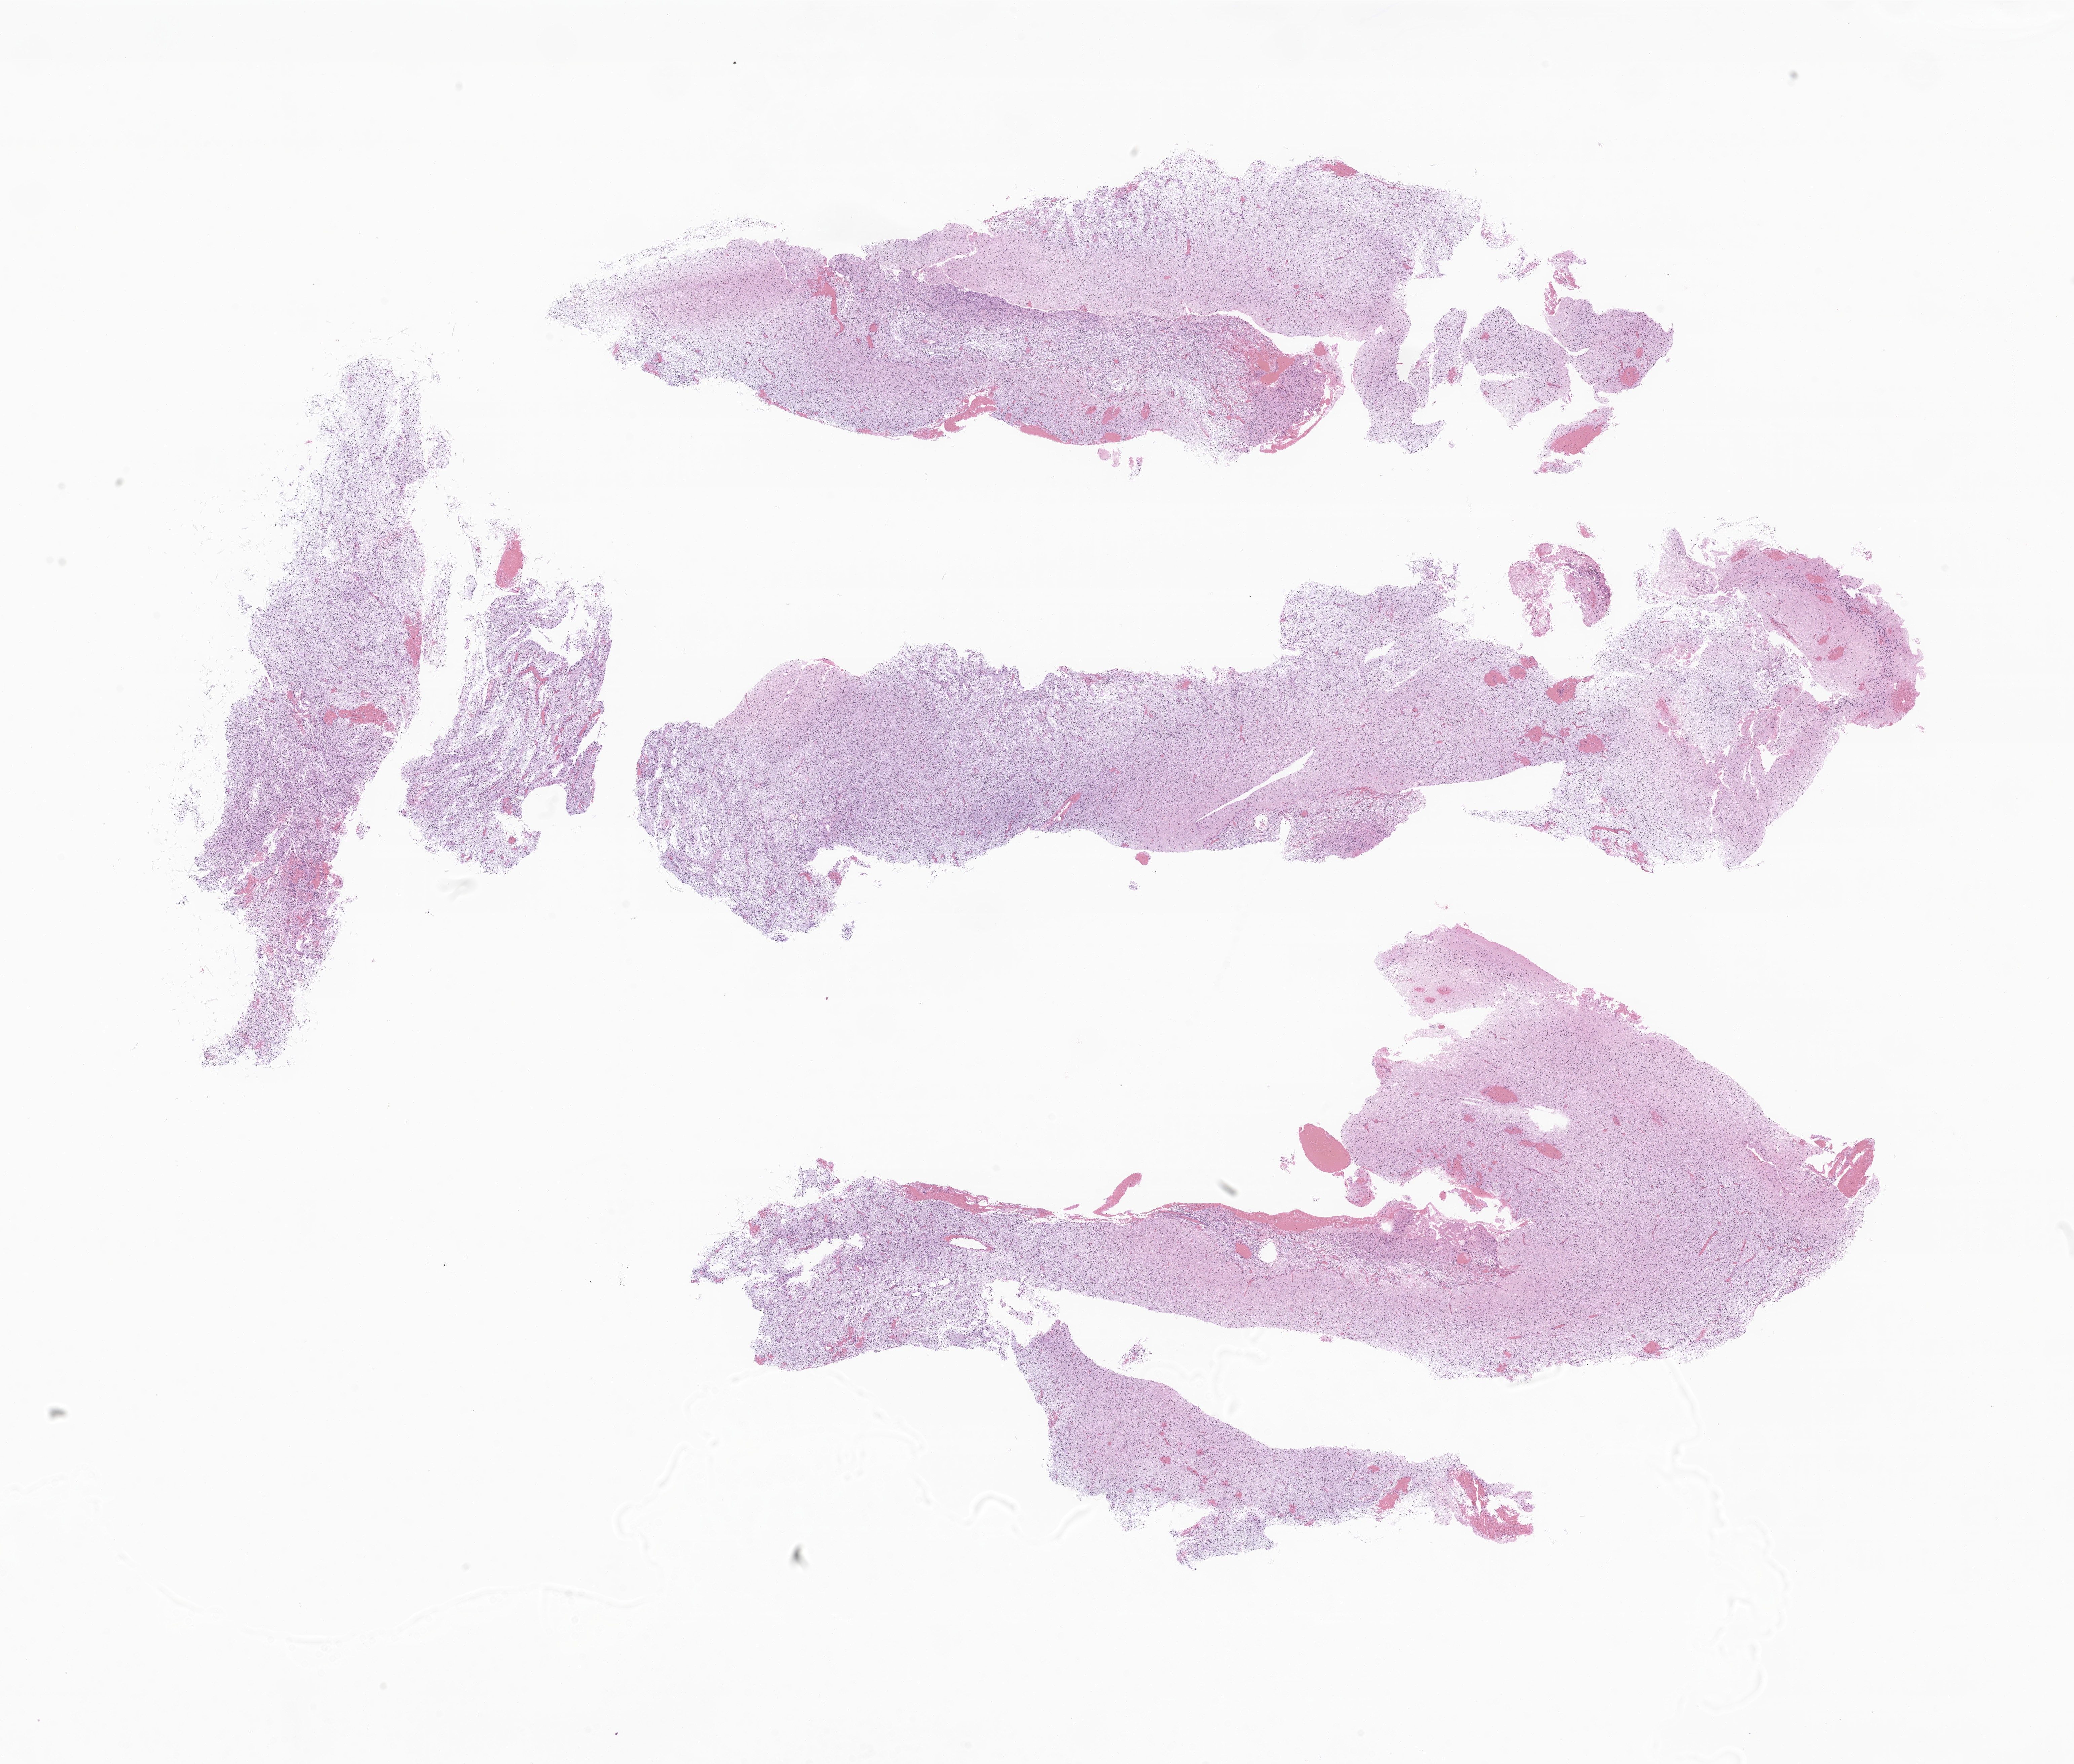
Digitized haematoxylin and eosin-stained section of tumor tissue from the brain — shown as a low-resolution overview of the whole scanned area (about 26.0 x 22.1 mm); FFPE section. Patient: female, age 707 days.
• recorded diagnosis: Pilocytic astrocytoma